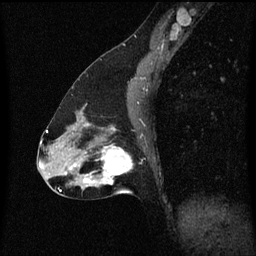
Breast MRI (dynamic contrast-enhanced), one sagittal slice; position 31 of 60 along the scan axis; dynamic contrast-enhanced series, image 2 of 3 at this slice position (ordered by acquisition); 1.5 T; TE 4.2 ms, TR 8.4 ms; 256 × 256 image matrix. Female patient, age 47 years.
Annotated regions visible in this slice (semi-automatically segmented with operator editing):
- analysis volume of interest (the breast-tissue region the enhancement analysis was run in; not a lesion): bounding box [x1, y1, x2, y2] px = [85, 136, 135, 195]
- tumour enhancement mask (voxels above the 70 % enhancement threshold inside the analysis volume of interest): [85, 146, 133, 185]